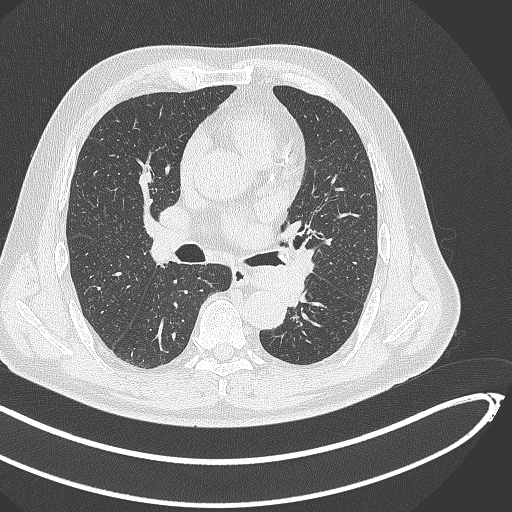
Chest CT, one axial slice; reconstruction kernel B70f; lung window (W 1500 / L -600 HU); 512 × 512 image matrix. Patient: male, 64 years. From the clinical record (not read from this slice): clinical TNM (as recorded): T1c N0 M0.
Annotated regions visible in this slice (bounding box drawn by a radiologist):
- lung tumour (recorded histology: squamous cell carcinoma): bounding box [x1, y1, x2, y2] px = [251, 252, 318, 308]